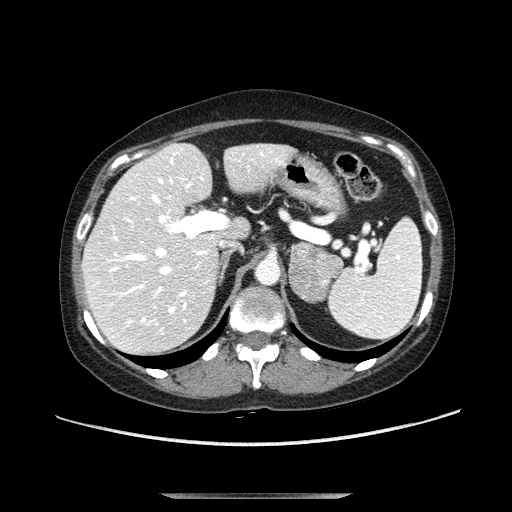
Contrast-enhanced abdominal CT, one axial slice; position 71 of 107 along the scan axis; soft-tissue window (W 400 / L 40 HU); 2.5 mm slice thickness; 512 × 512 image matrix, field of view 380 × 380 mm. Female patient. From the clinical record (not read from this slice): diagnosis: adrenocortical carcinoma; tumour side: left adrenal; tumour size at pathology: 7.5 cm; Ki-67 index: 9 %; stage (as recorded): 3.
Structures marked on this image (semi-automatically segmented with operator editing):
- mass: box from (x=289, y=242) to (x=344, y=300) px